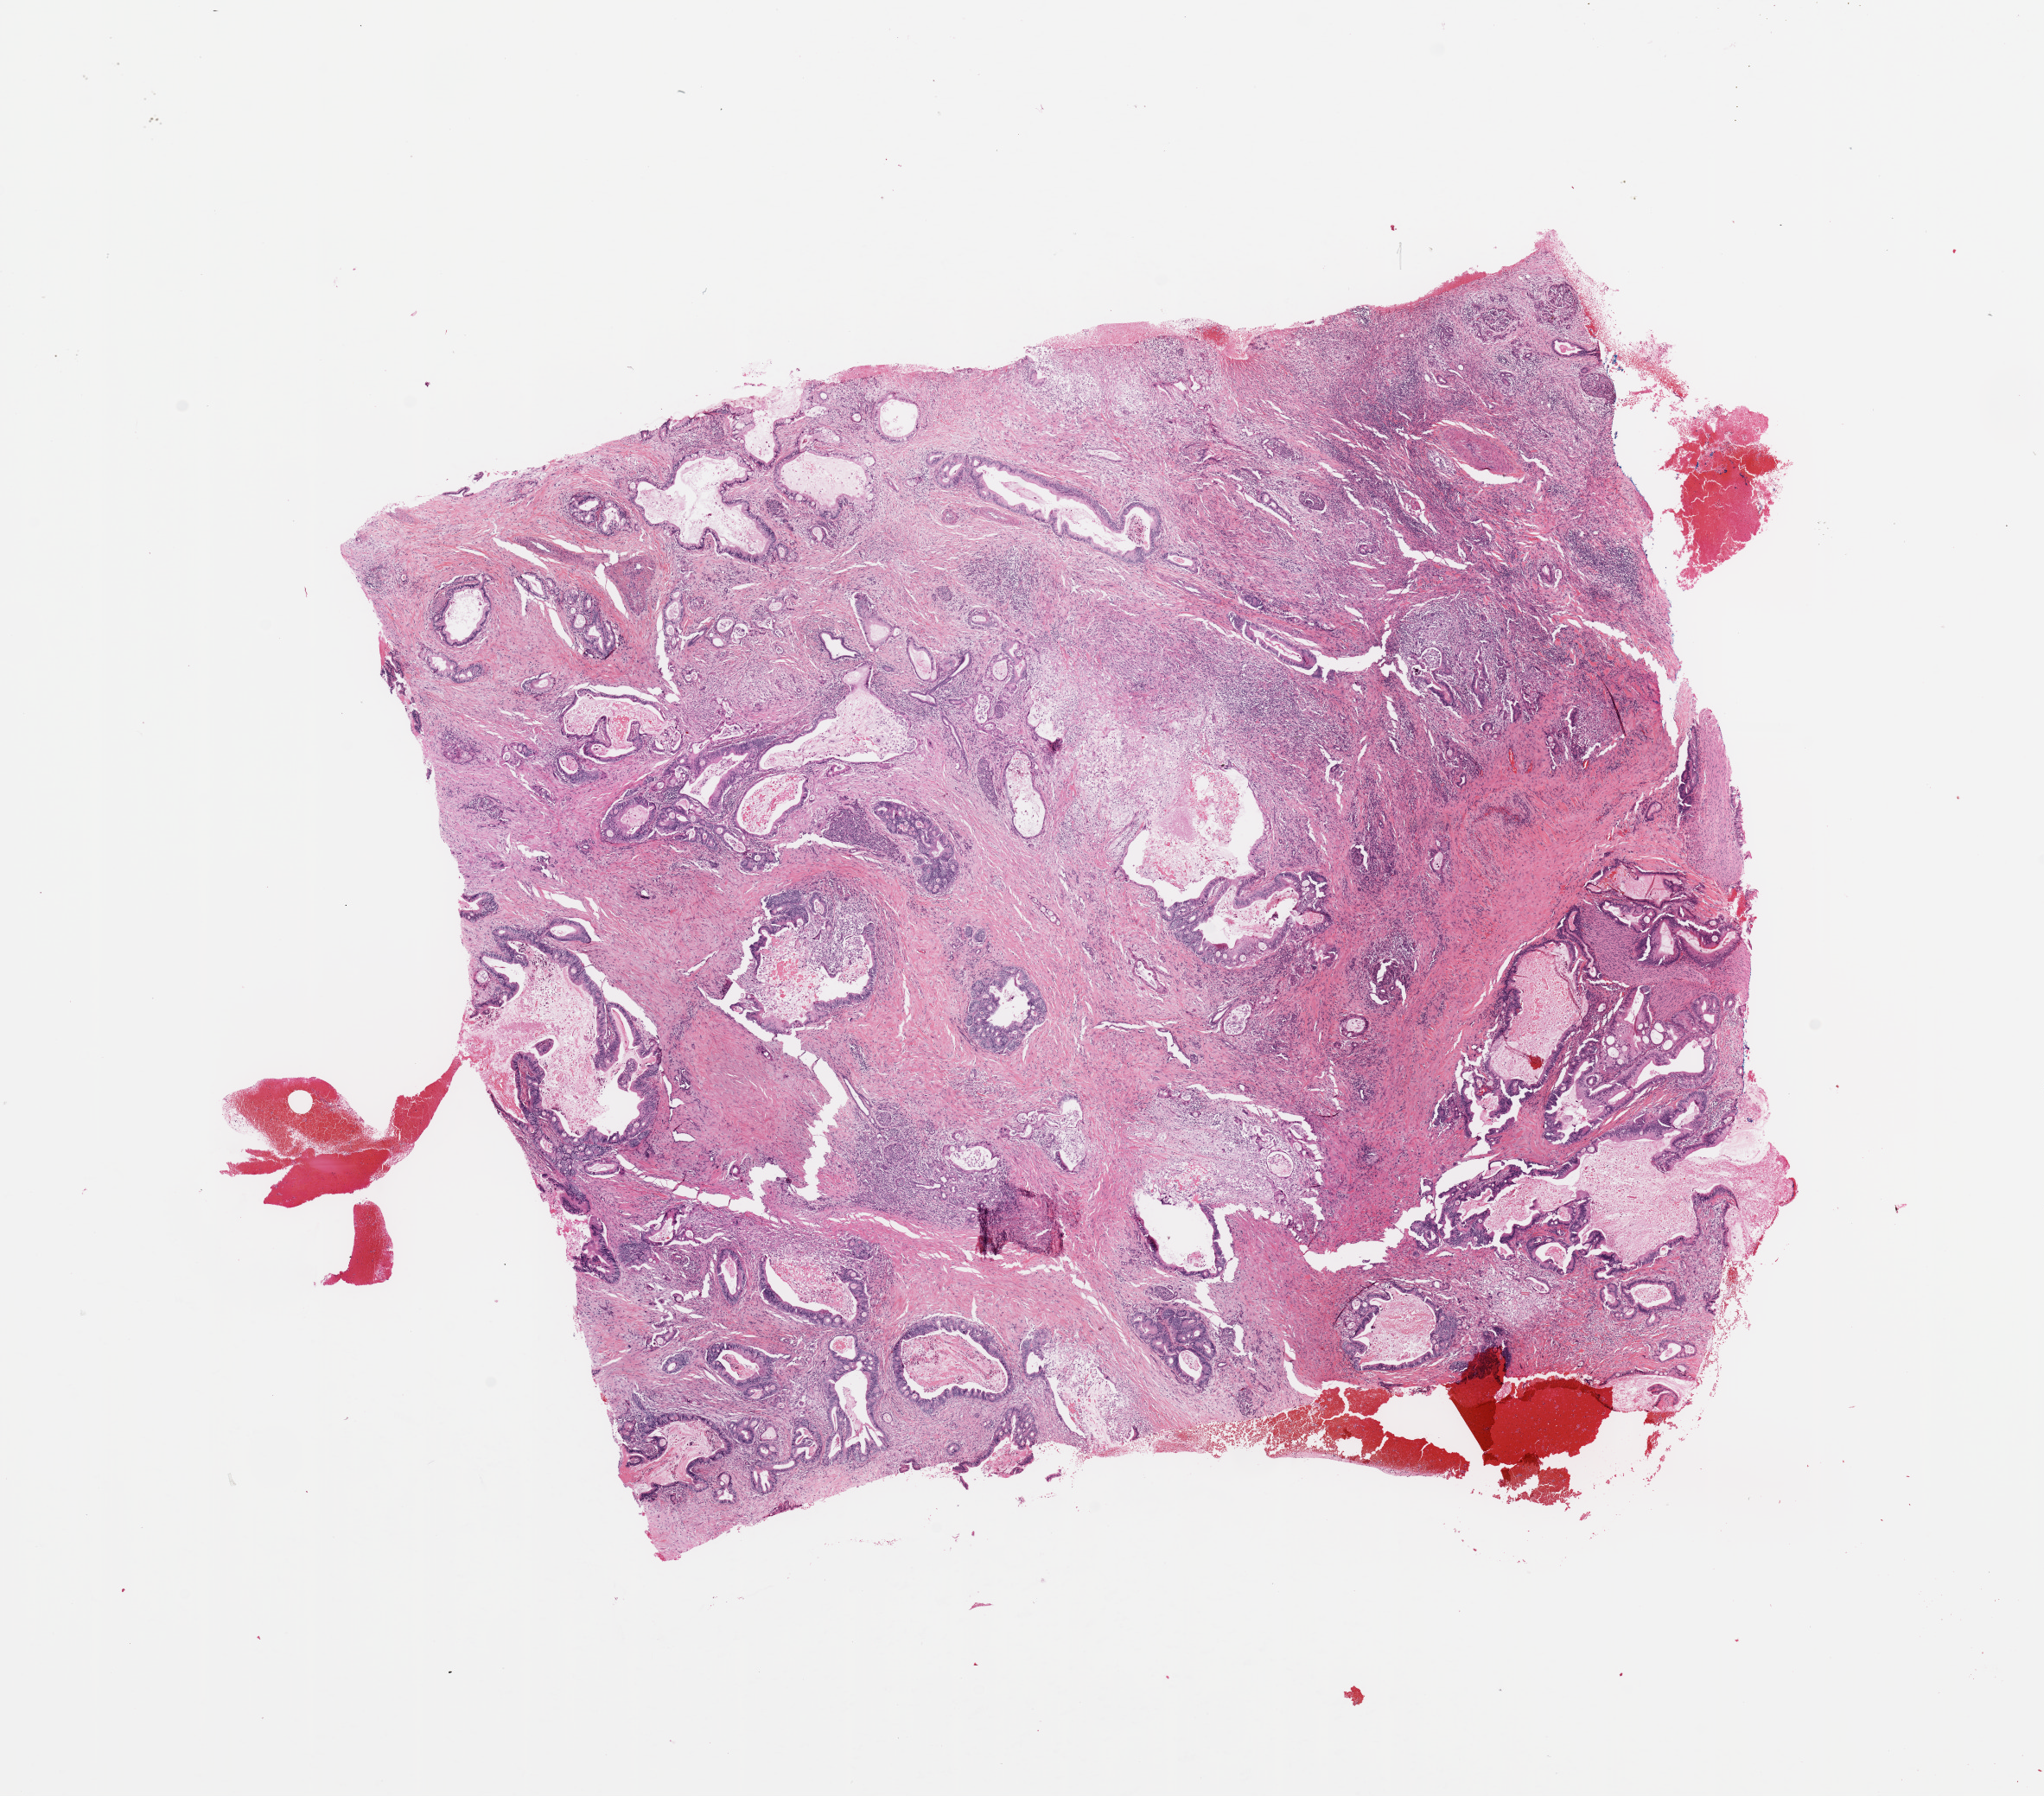
H&E-stained whole-slide image, low-resolution overview of the scanned area, about 18.7 x 16.4 mm (acquisition: 20x scan). Pancreas, tumour tissue. Female, 64 y/o. Histologic grade: G2 (moderately differentiated).
AJCC pathologic stage: IIA. Diagnosis: Infiltrating duct carcinoma, NOS.